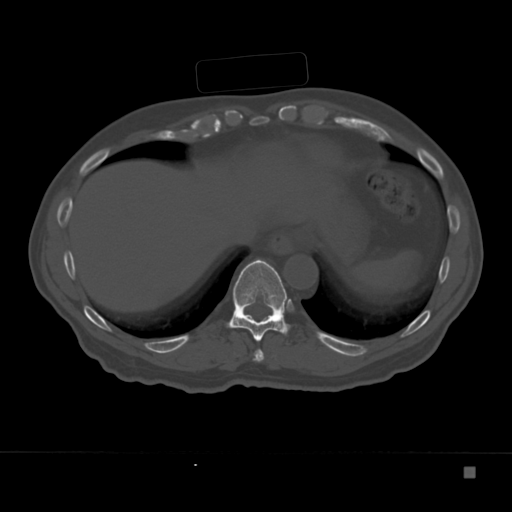
CT including the spine, one axial slice; slice 172 of 332 in the series (ordered by position); reconstruction kernel Br40s; 120 kVp; bone window (W 1800 / L 400 HU); 1.5 mm slice thickness; 512 × 512 image matrix, field of view 389 × 389 mm. Patient: male, 72 years. Case-level facts recorded for this patient, not image findings: primary cancer: skeletal.
Outlined on this slice (semi-automatic segmentation, software-assisted and operator-edited):
- T10 vertebra: bounding box <227,259,290,342> (left, top, right, bottom; pixels)
- T9 vertebra: <253,349,264,362>